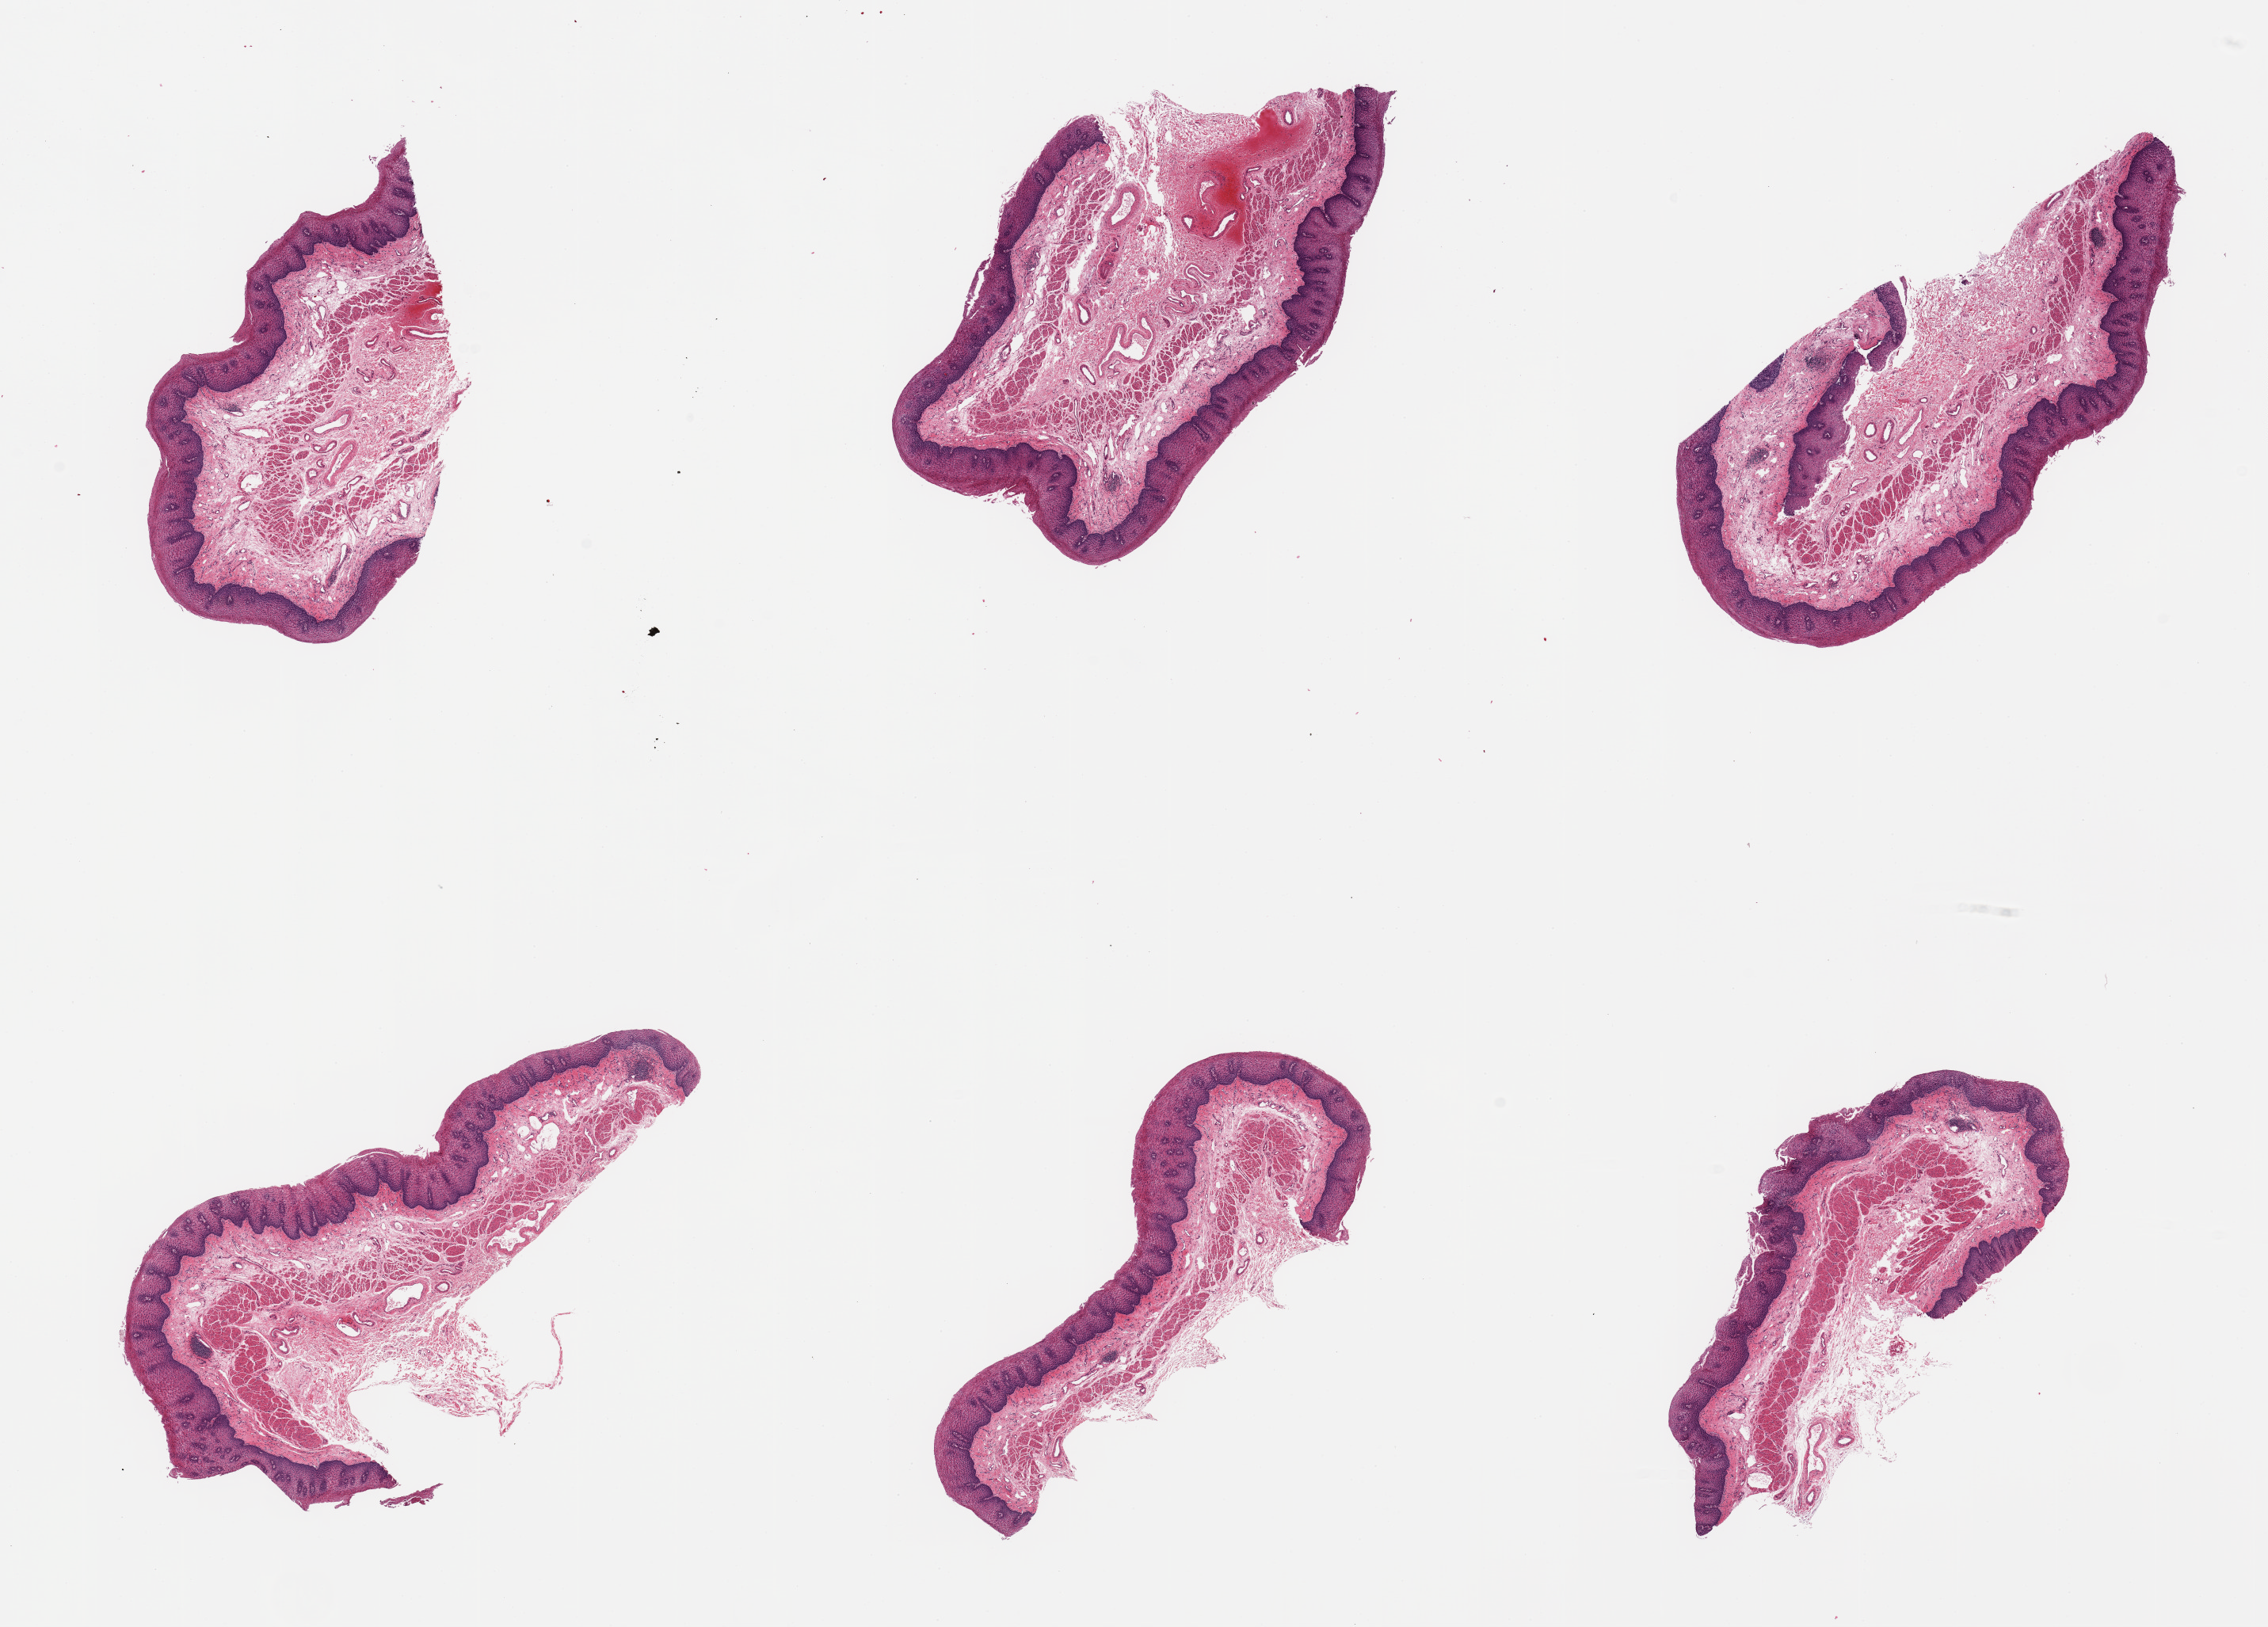
Whole-slide image, haematoxylin and eosin stain, shown as a low-resolution overview of the whole scanned area (about 22.6 x 16.2 mm), PAXgene-fixed paraffin-embedded (PFPE) section, target tissue: esophageal mucous membrane, tissue donor sample.
• pathologist's review note for this sample: 6 pieces, squamous mucosa is ~0.5mm, ~20-25% thickness